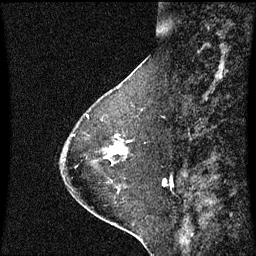
Breast MRI (dynamic contrast-enhanced), one sagittal slice; slice 19 of 60 in the series (ordered by position); dynamic contrast-enhanced series, image 2 of 3 at this slice position (ordered by acquisition); 1.5 T; TE 4.2 ms, TR 8.9 ms; 2 mm slice thickness; 256 × 256 image matrix. Patient: female, 63 years. Case-level facts recorded for this patient, not image findings: setting: breast cancer imaged before/during neoadjuvant chemotherapy; receptor status: HR-positive, HER2-negative.
Annotated regions visible in this slice (semi-automatically segmented with operator editing):
- analysis volume of interest (the breast-tissue region the enhancement analysis was run in; not a lesion): bounding box [x1, y1, x2, y2] px = [106, 142, 125, 165]
- tumour enhancement mask (voxels above the 70 % enhancement threshold inside the analysis volume of interest): [110, 144, 125, 157]